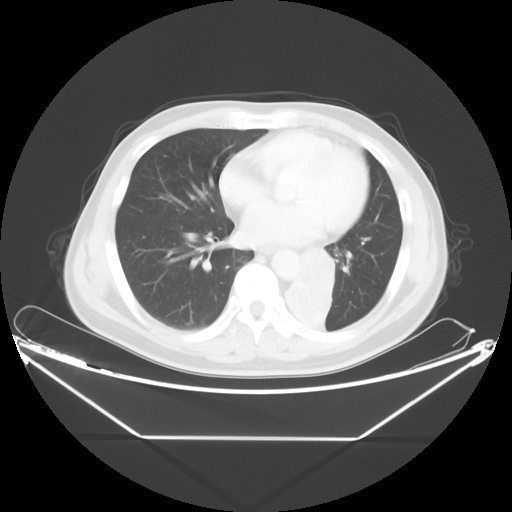
Chest CT, one axial slice; reconstruction kernel STANDARD; lung window (W 1500 / L -600 HU); 5 mm slice thickness; 512 × 512 image matrix, field of view 438 × 438 mm. Male patient, age 58 years. From the clinical record (not read from this slice): clinical TNM (as recorded): T3 N3 M0.
Structures marked on this image (rectangle marked by the reading radiologist):
- lung tumour (recorded histology: squamous cell carcinoma): box from (x=279, y=244) to (x=349, y=343) px